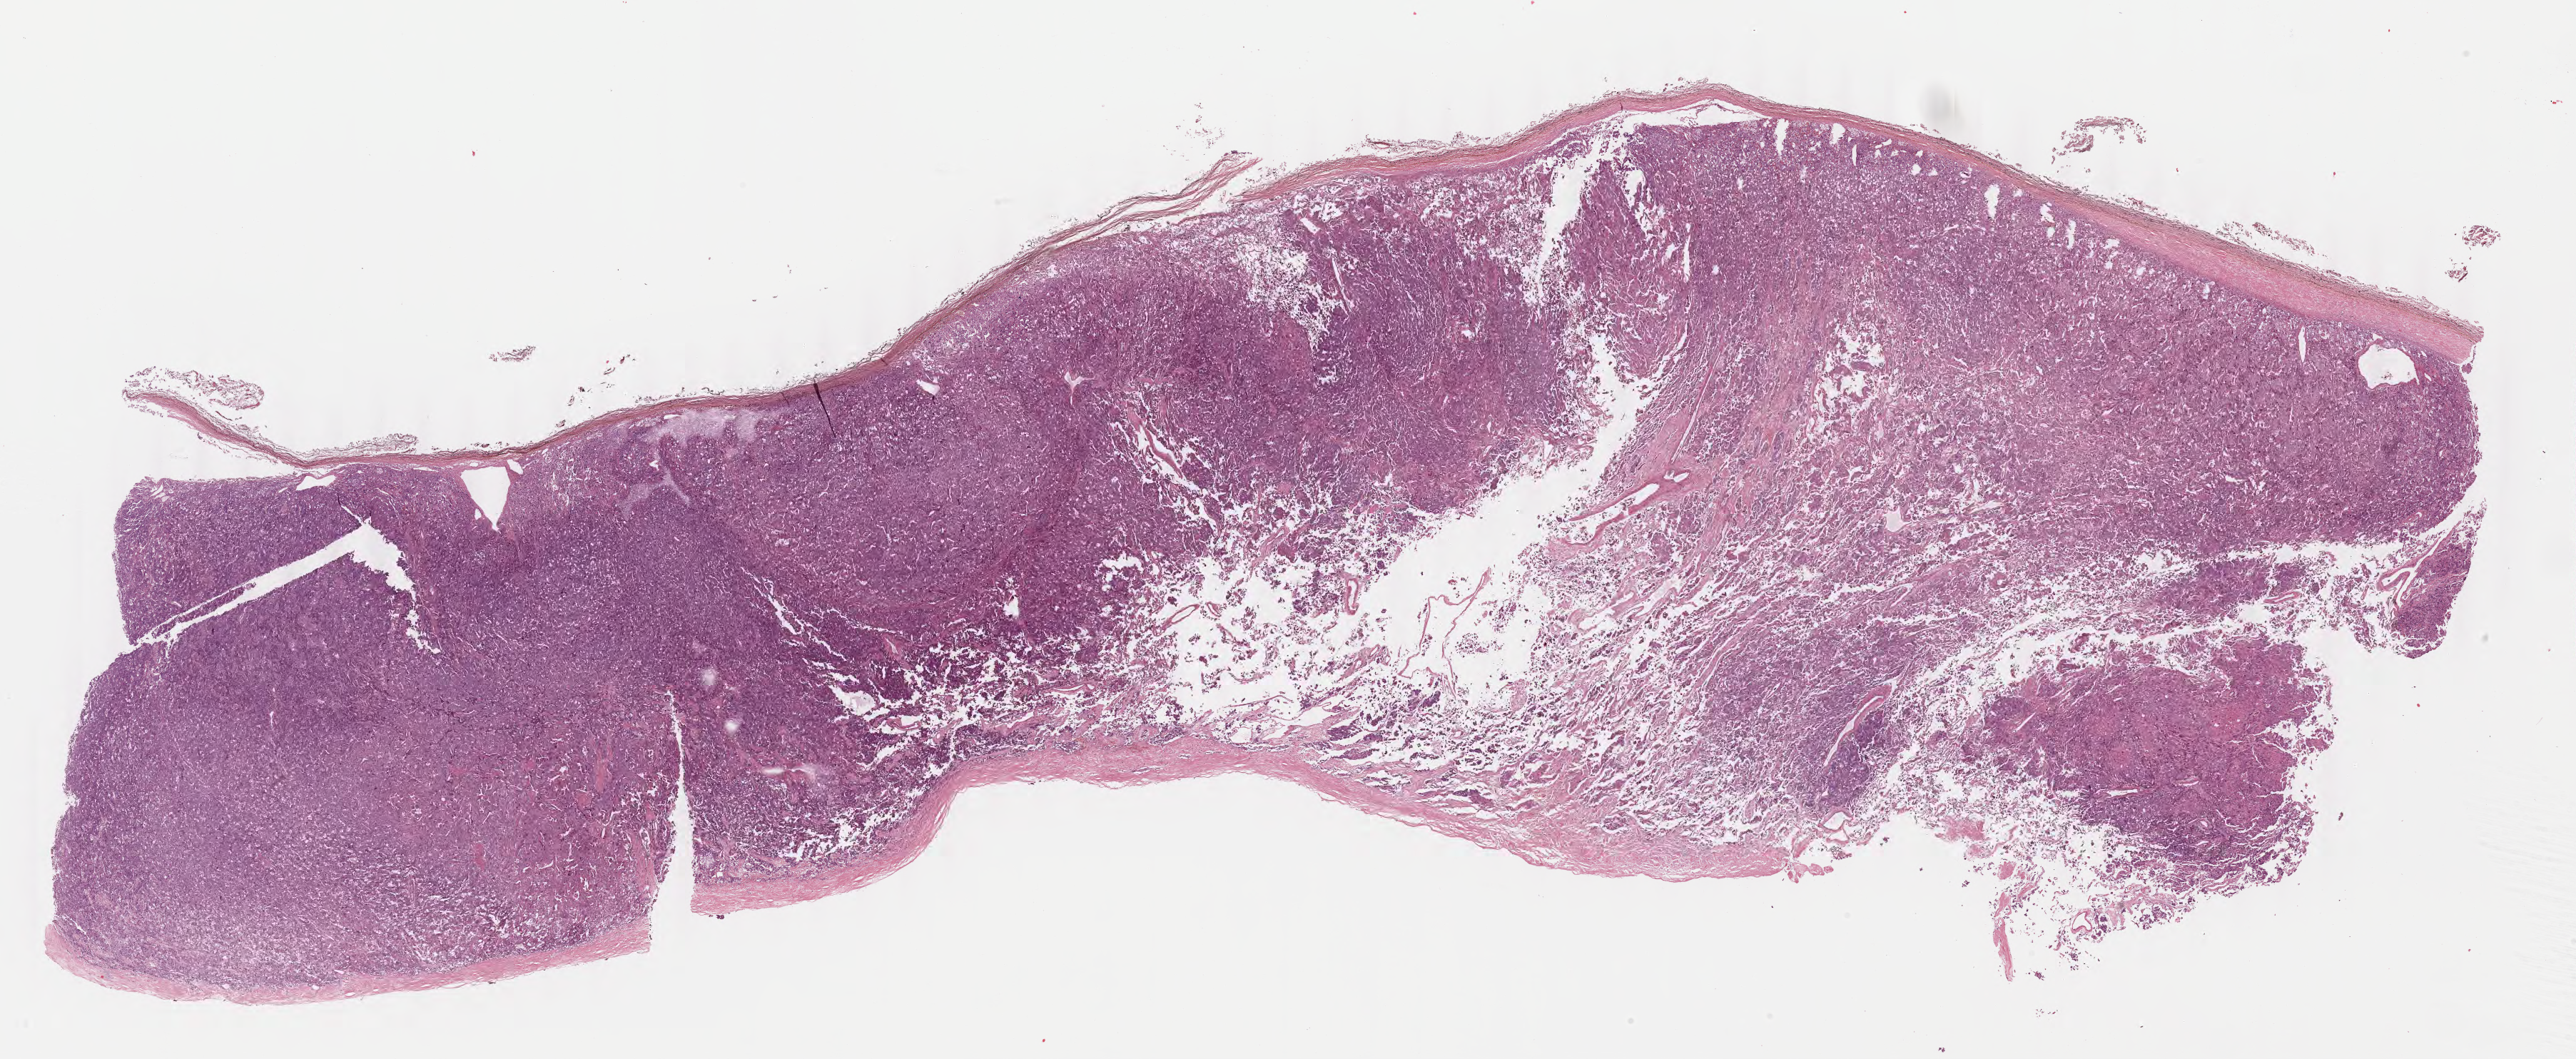
Whole-slide histology image, H&E, whole scanned area (about 28.5 x 11.7 mm, from a 40x scan) shown as a low-resolution overview, FFPE section, sample: primary tumour, adrenal gland. Female, age 64 years at initial diagnosis.
Pathologic diagnosis: Pheochromocytoma, NOS. Laterality: right.